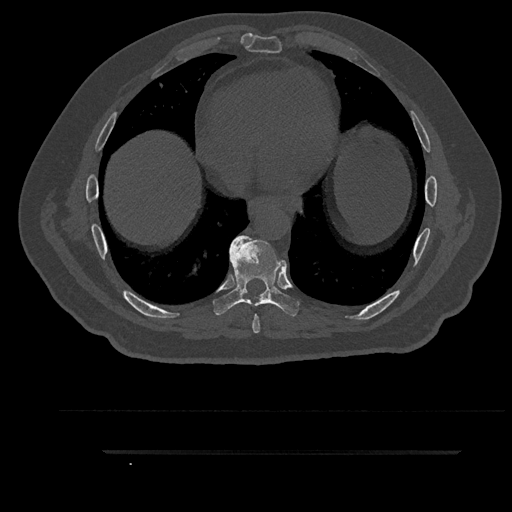
CT including the spine, one axial slice. Position 488 of 797 along the scan axis. 120 kVp. Bone window (W 1800 / L 400 HU). 0.5 mm slice thickness. 512 × 512 image matrix, field of view 432 × 432 mm. Male patient, age 63 years. From the clinical record (not read from this slice): primary cancer: renal; vertebrae with lytic lesions (as recorded): T8.
Annotated regions visible in this slice (semi-automatically segmented with operator editing):
- T7 vertebra: bounding box <252,315,260,334> (left, top, right, bottom; pixels)
- T8 vertebra: <213,235,299,316>